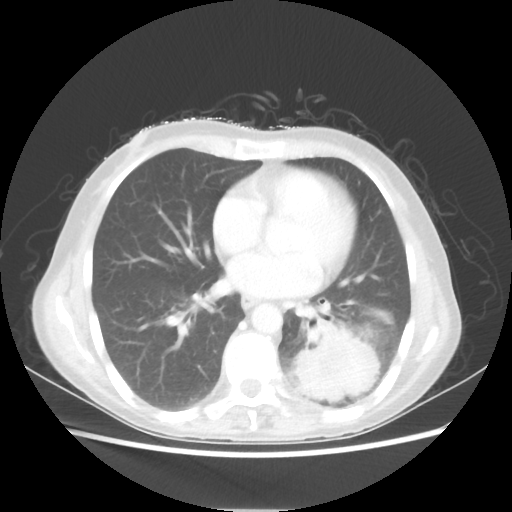
Chest CT, one axial slice; position 25 of 56 along the scan axis; reconstruction kernel STANDARD; 80 kVp; lung window (W 1500 / L -600 HU); 5 mm slice thickness; 512 × 512 image matrix, field of view 360 × 360 mm. Female patient, age 53 years. Case-level facts recorded for this patient, not image findings: clinical TNM (as recorded): T3 N0 M0.
Outlined on this slice (rectangle marked by the reading radiologist):
- lung tumour (recorded histology: adenocarcinoma): bounding box (x1, y1, x2, y2) in pixels: (292, 321, 380, 401)